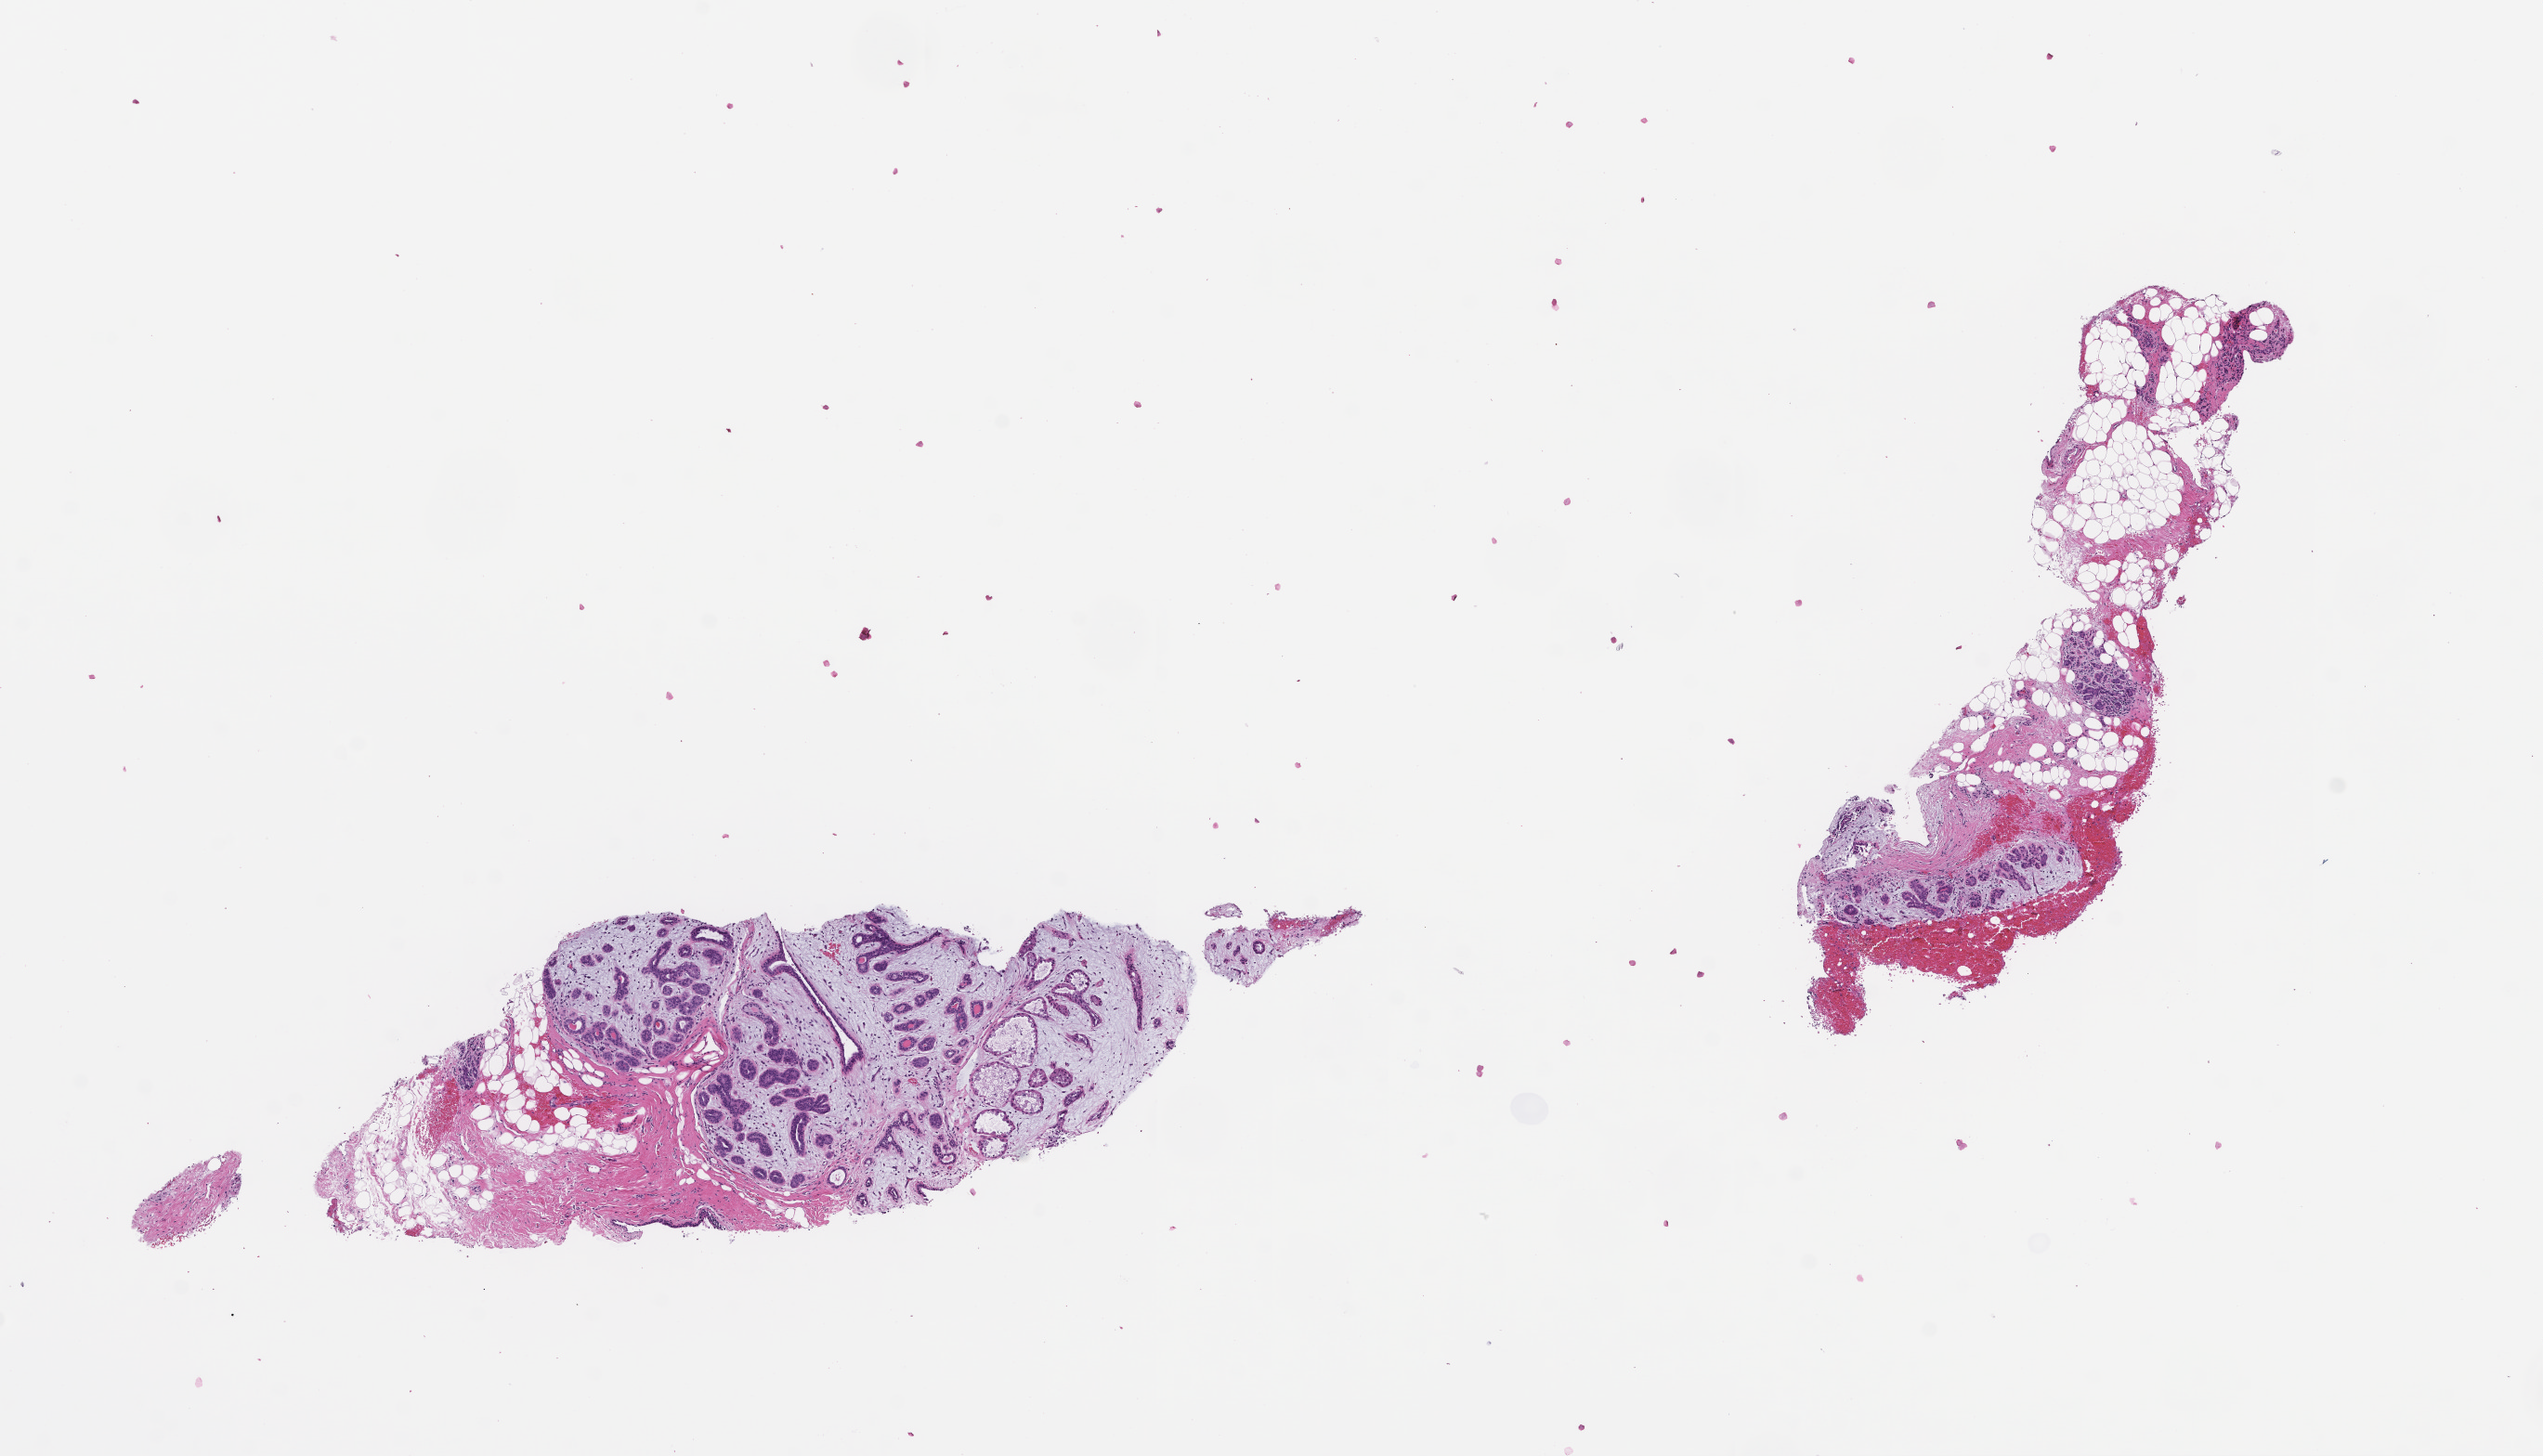
Digitized hematoxylin and eosin (H&E)-stained section, whole scanned area (about 11.1 x 6.3 mm) shown as a low-resolution overview; formalin-fixed paraffin-embedded section; site: ovary; specimen time point: collected at baseline (before treatment). Patient: female.
This section: primary tumor. Diagnosis: Ovarian Carcinoma.